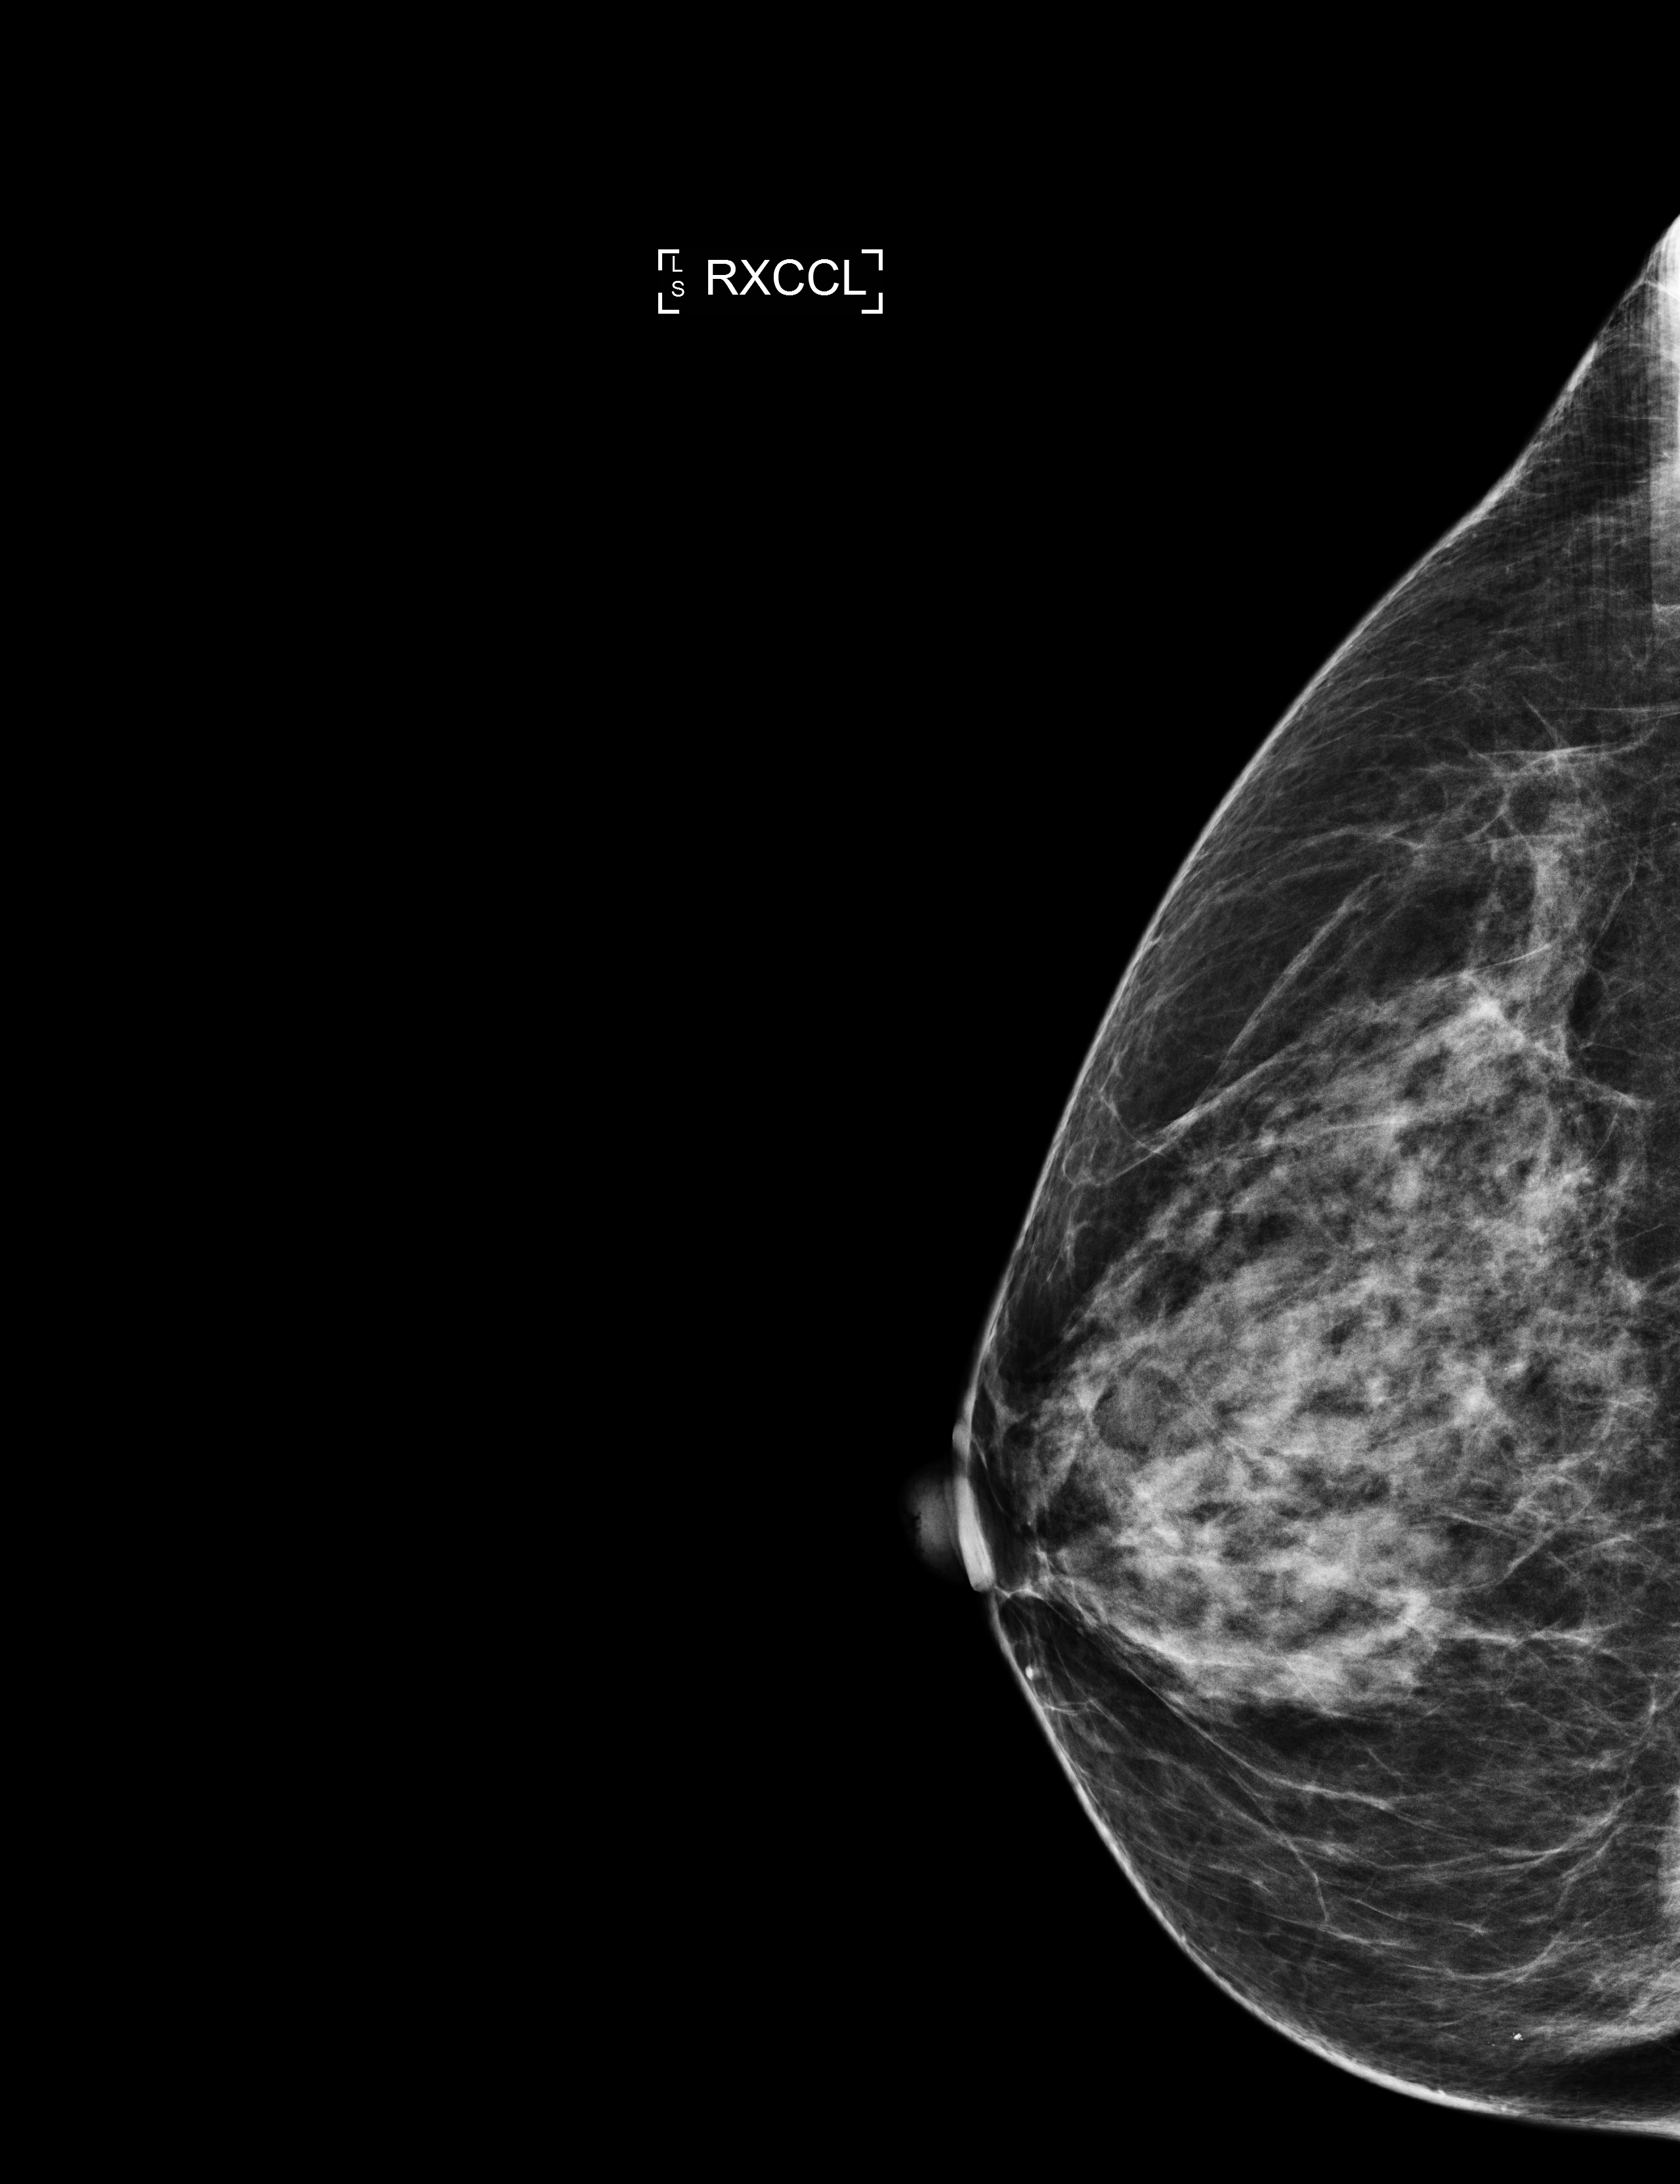
Annual screening mammography examination; compressed breast thickness 58 mm. Female patient, age 61 years.
Image type: full-field digital mammogram. Breast: right. Projection: exaggerated CC view (lateral).